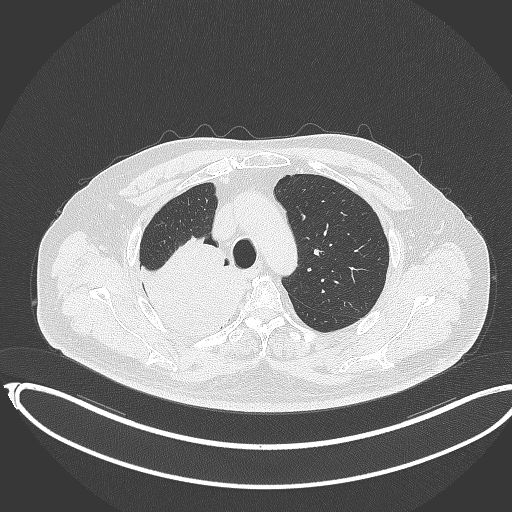
Chest CT, one axial slice; slice 281 of 403 in the series (ordered by position); reconstruction kernel B70f; 120 kVp; lung window (W 1500 / L -600 HU); 512 × 512 image matrix. Patient: male, 68 years. From the clinical record (not read from this slice): clinical TNM (as recorded): T2a N0 M0.
Annotated regions visible in this slice (bounding box drawn by a radiologist):
- lung tumour (recorded histology: adenocarcinoma): bounding box (x1, y1, x2, y2) in pixels: (127, 230, 251, 350)